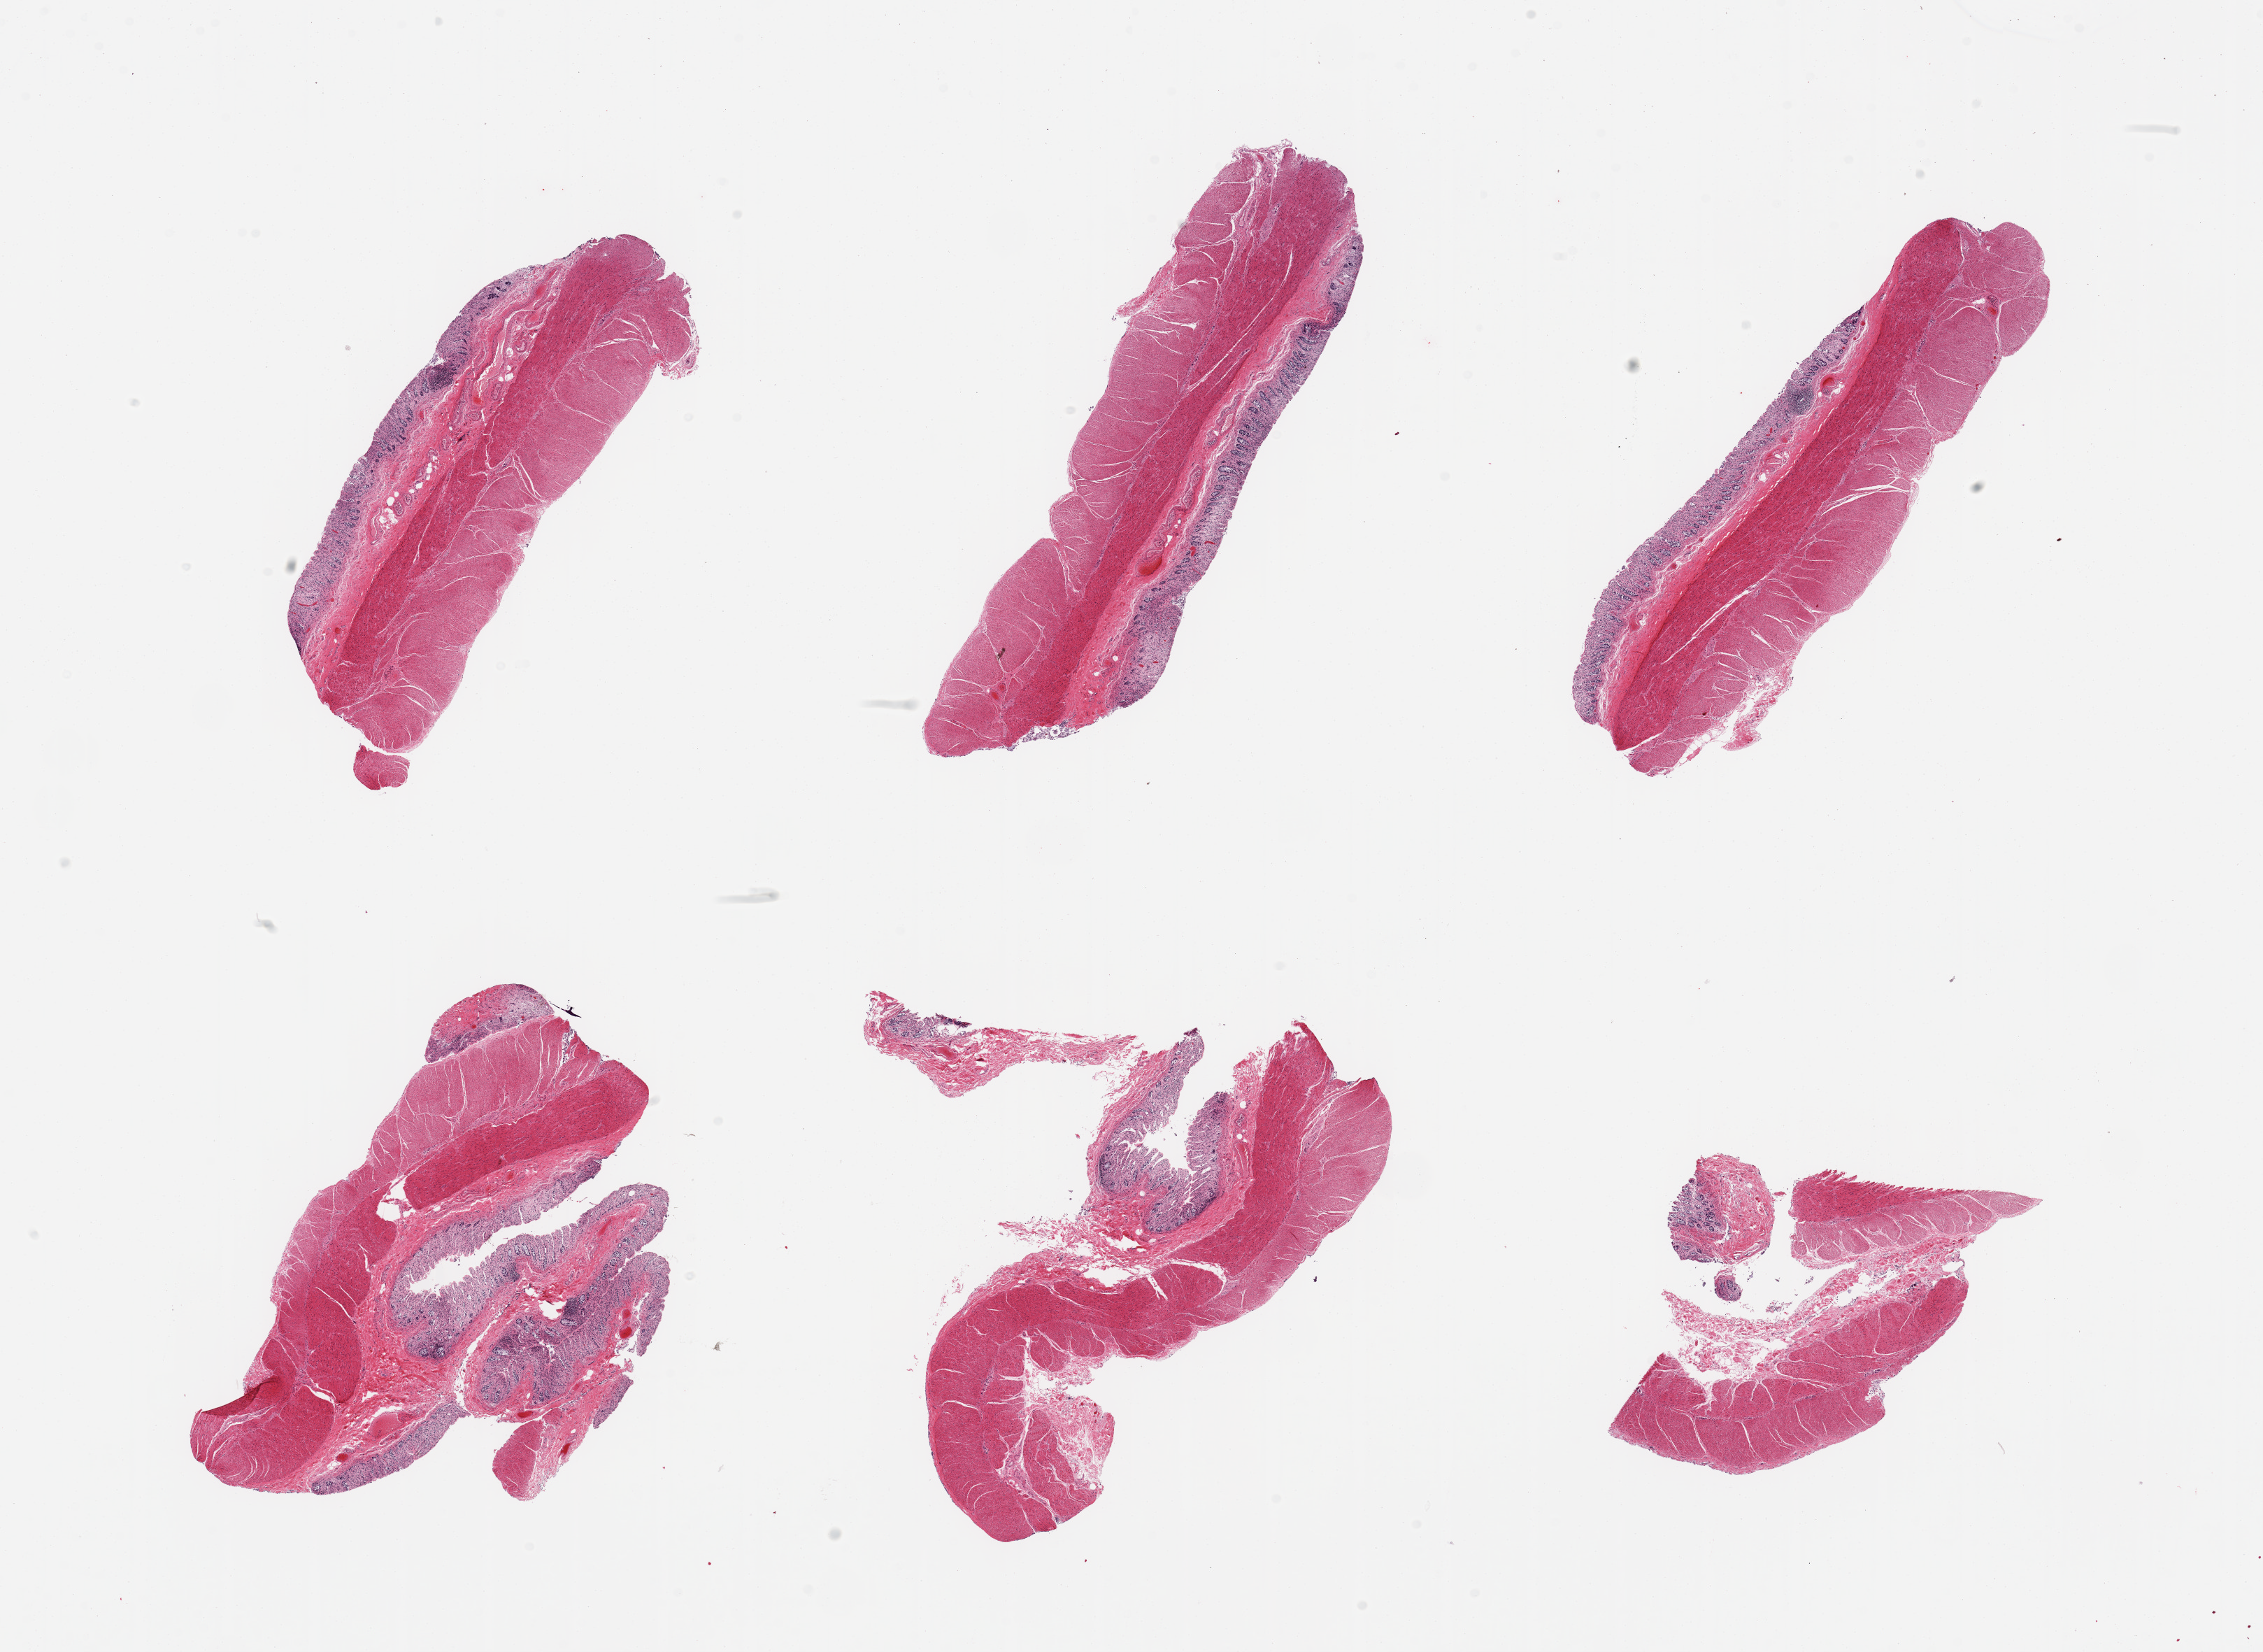
Digitized H&E-stained section, whole scanned area (about 25.6 x 18.7 mm) shown as a low-resolution overview; PAXgene-fixed paraffin-embedded (PFPE) section; target tissue: sigmoid colon; tissue donor sample.
Reviewer comment on this tissue sample: 6 pieces; mucosa severely autolyzed, muscularis intact.